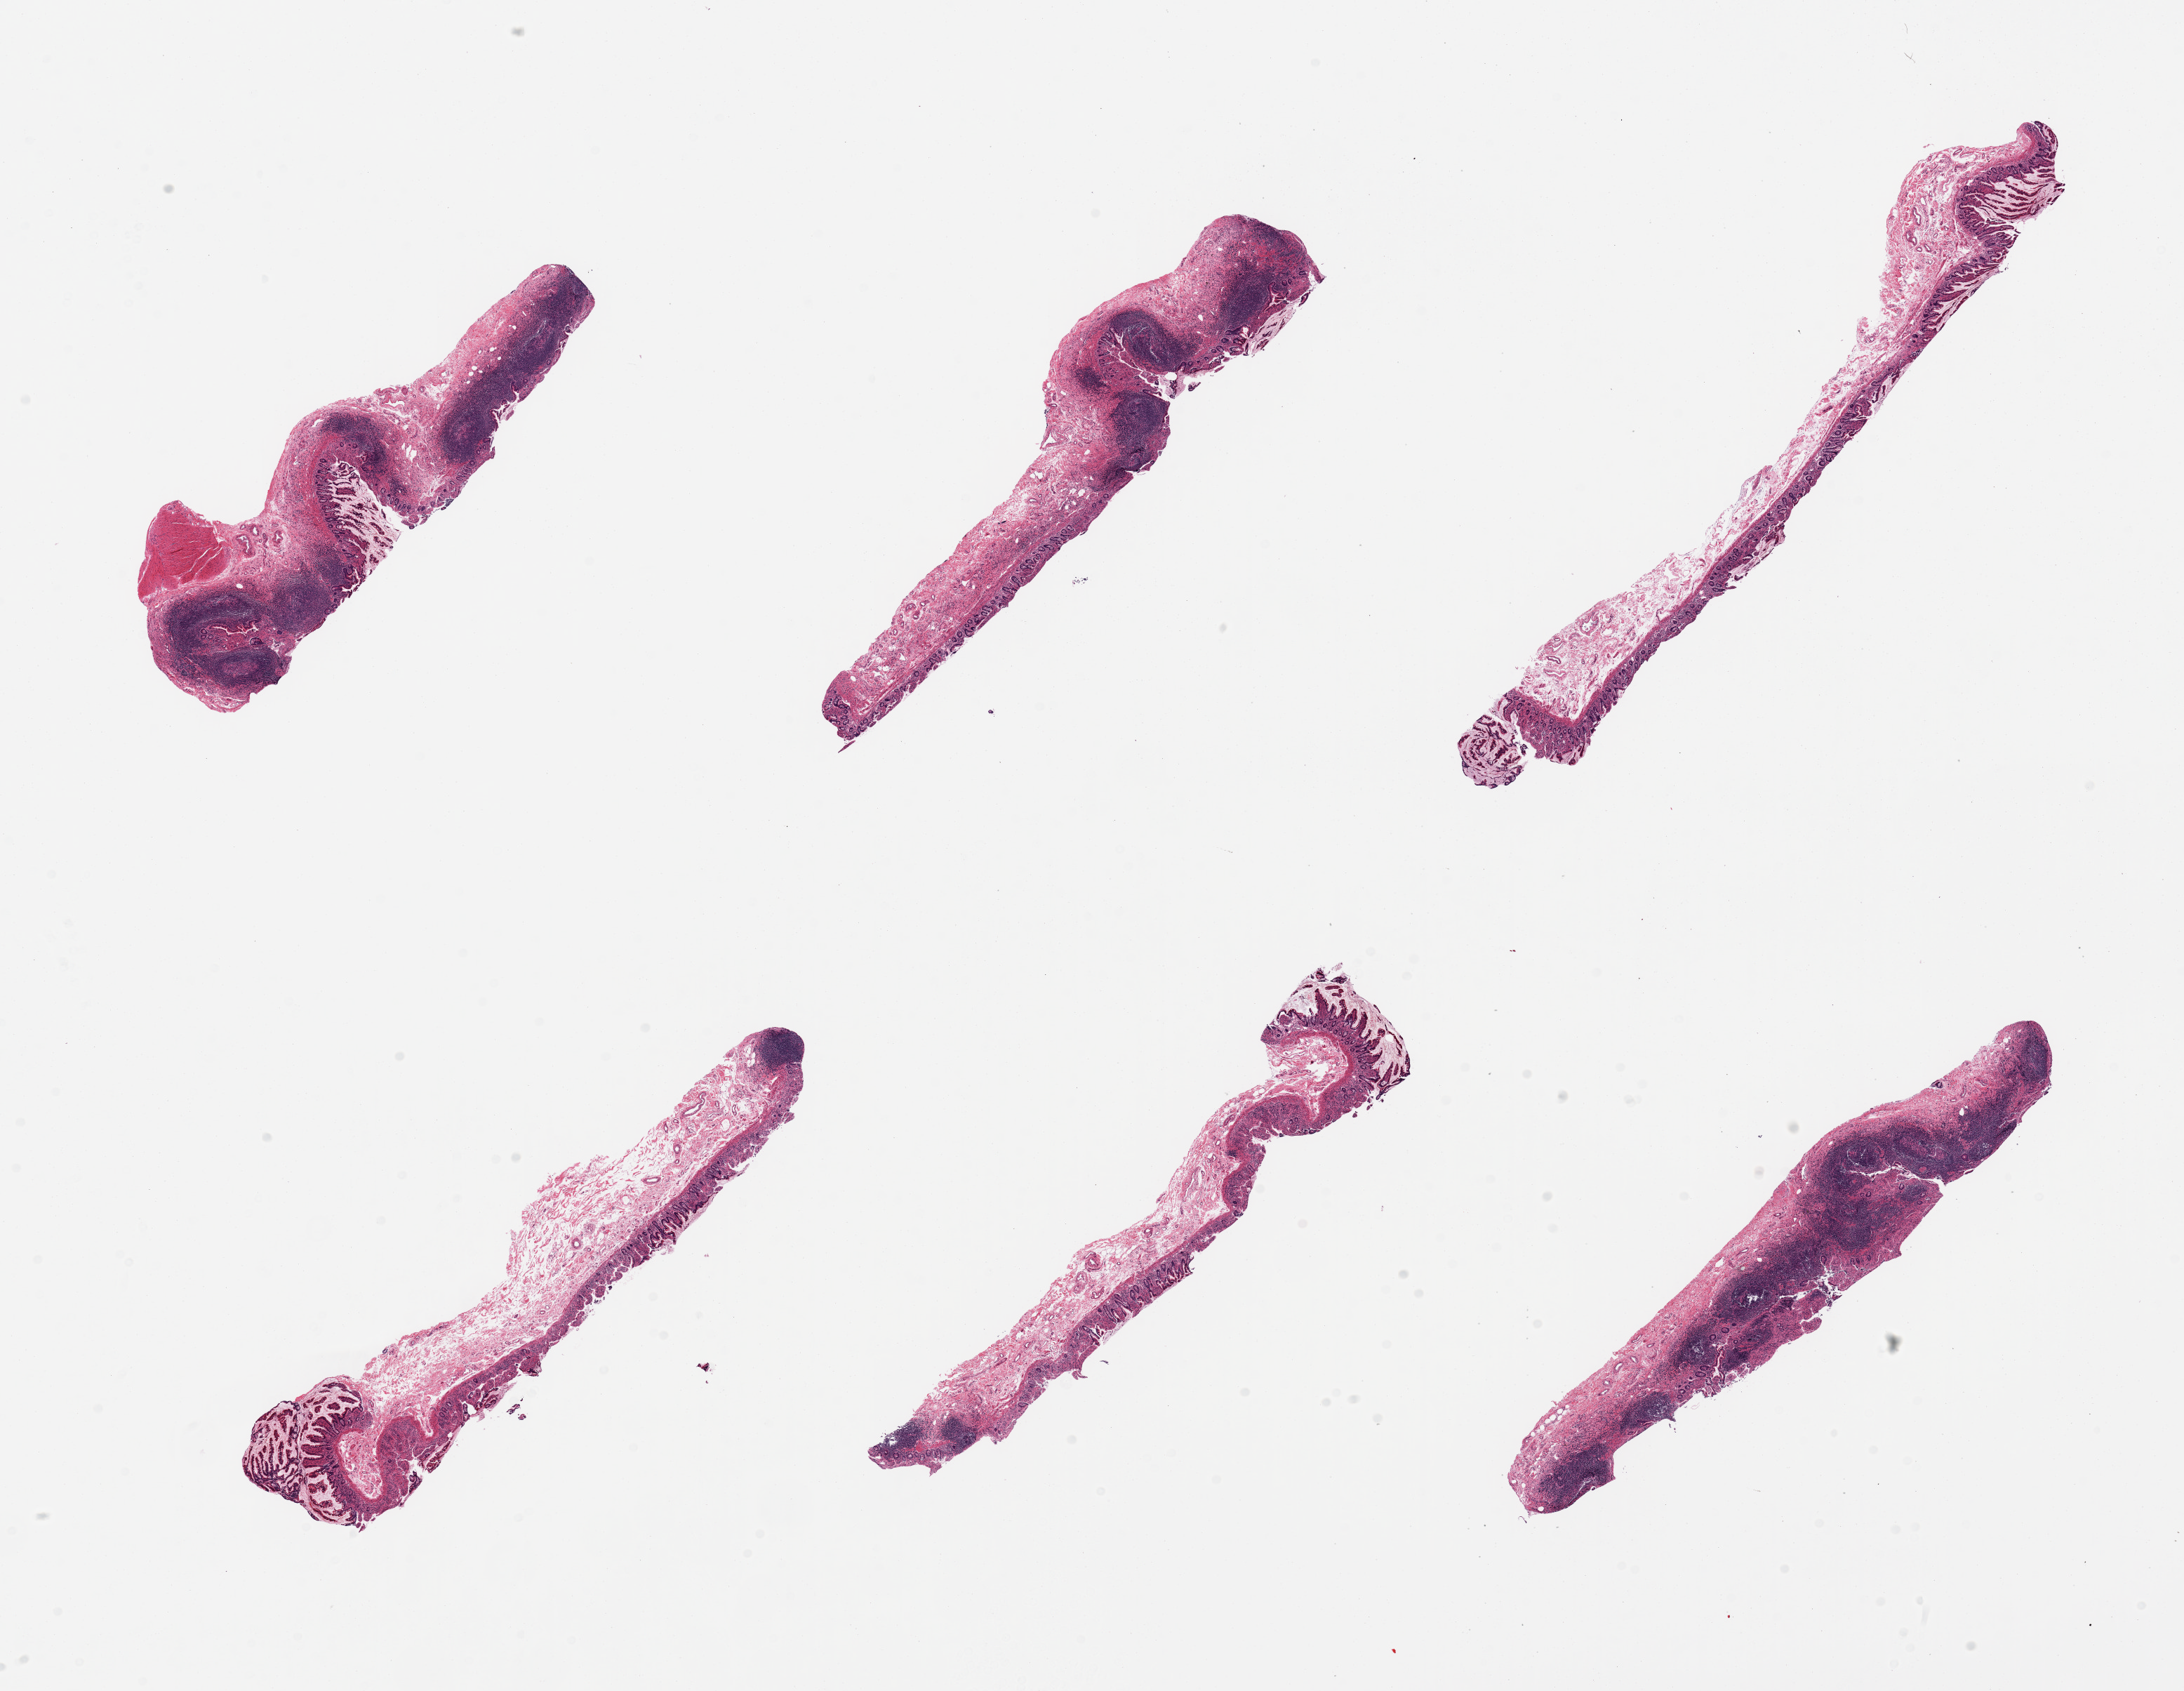
Whole-slide image, haematoxylin and eosin stain, brightfield — low-resolution overview of the scanned area, about 24.6 x 19.1 mm (from a 20x scan); PAXgene-fixed paraffin-embedded (PFPE) section; section of ileum (target tissue); donor tissue sample. Male donor.
Pathologist's review note for this sample: 6 pieces, well preserved, good lymphoid aggregates, ~40% total tisssue.